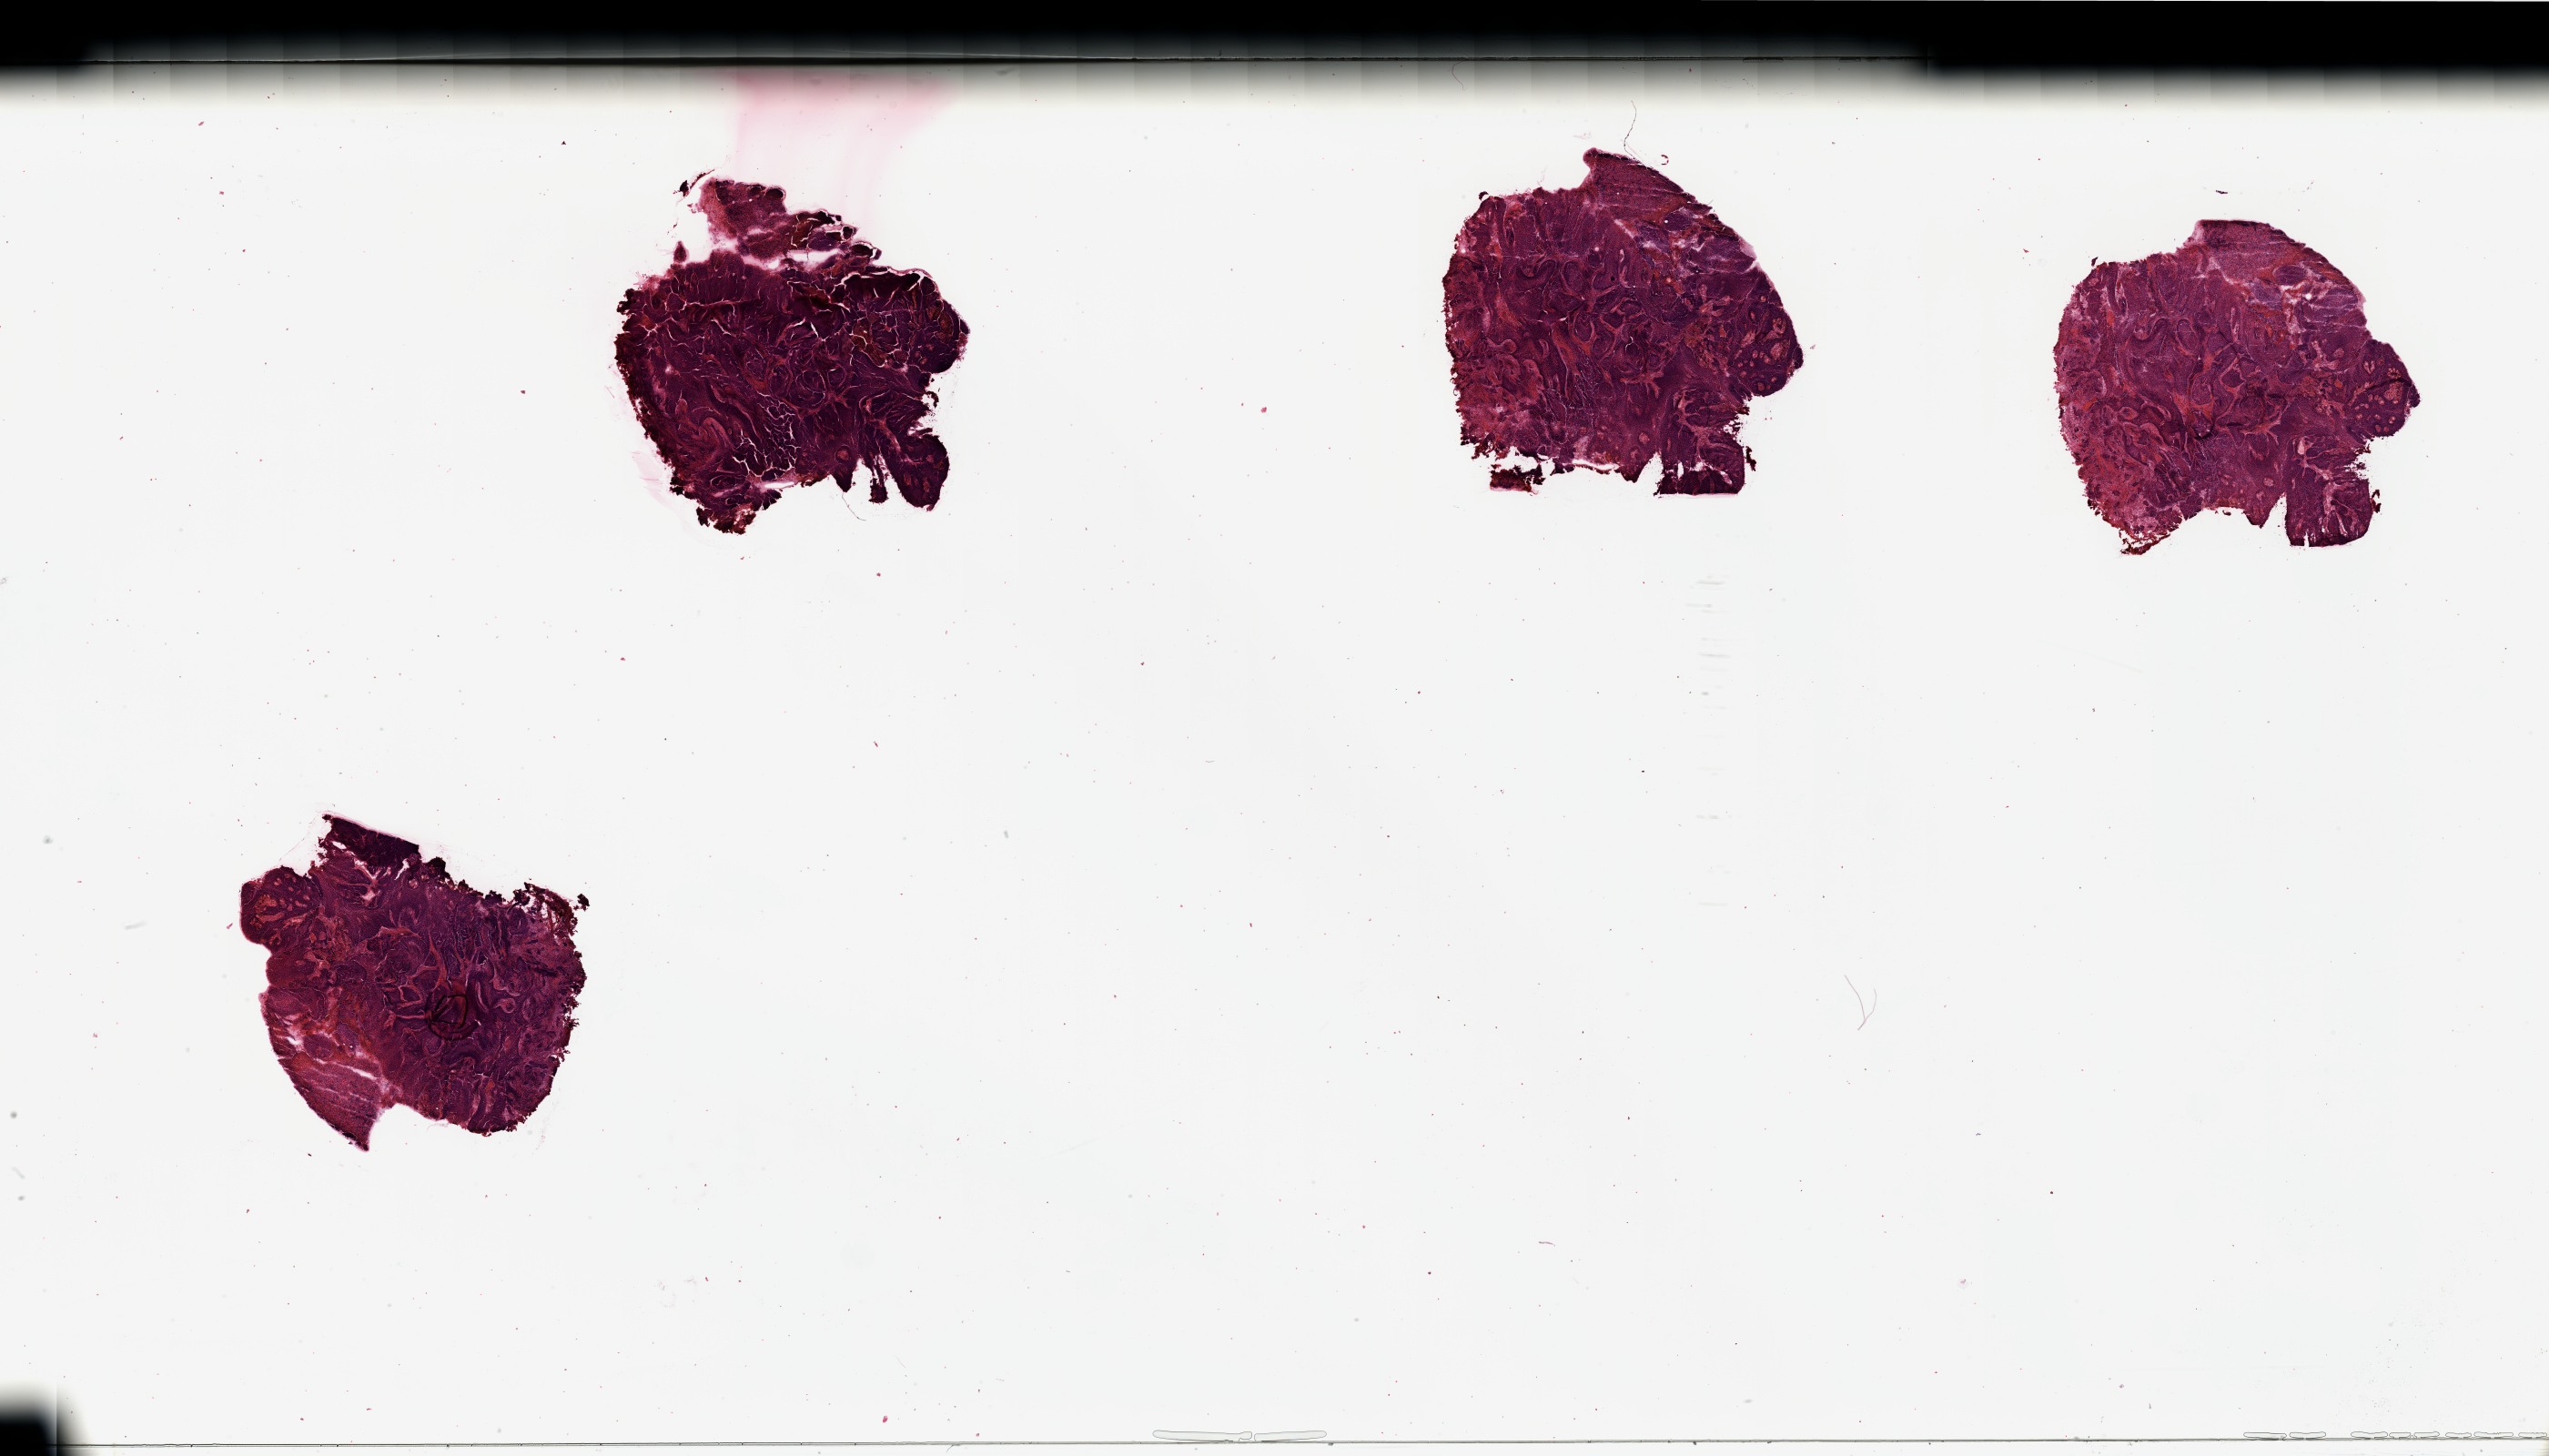
Digitized Hematoxylin and eosin (H&E) stained tissue section (whole slide), low-resolution overview of the scanned area, about 44.3 x 25.3 mm (slide scanned at 20x), tumour tissue sample, sampled site: oral cavity. Patient: male, age 63 years. Histologic grade: G2 (moderately differentiated). Pathologist review of this section (percent, as recorded): tumour nuclei 95%, necrosis 15%.
Diagnosis: Squamous cell carcinoma, NOS. AJCC pathologic stage: III.